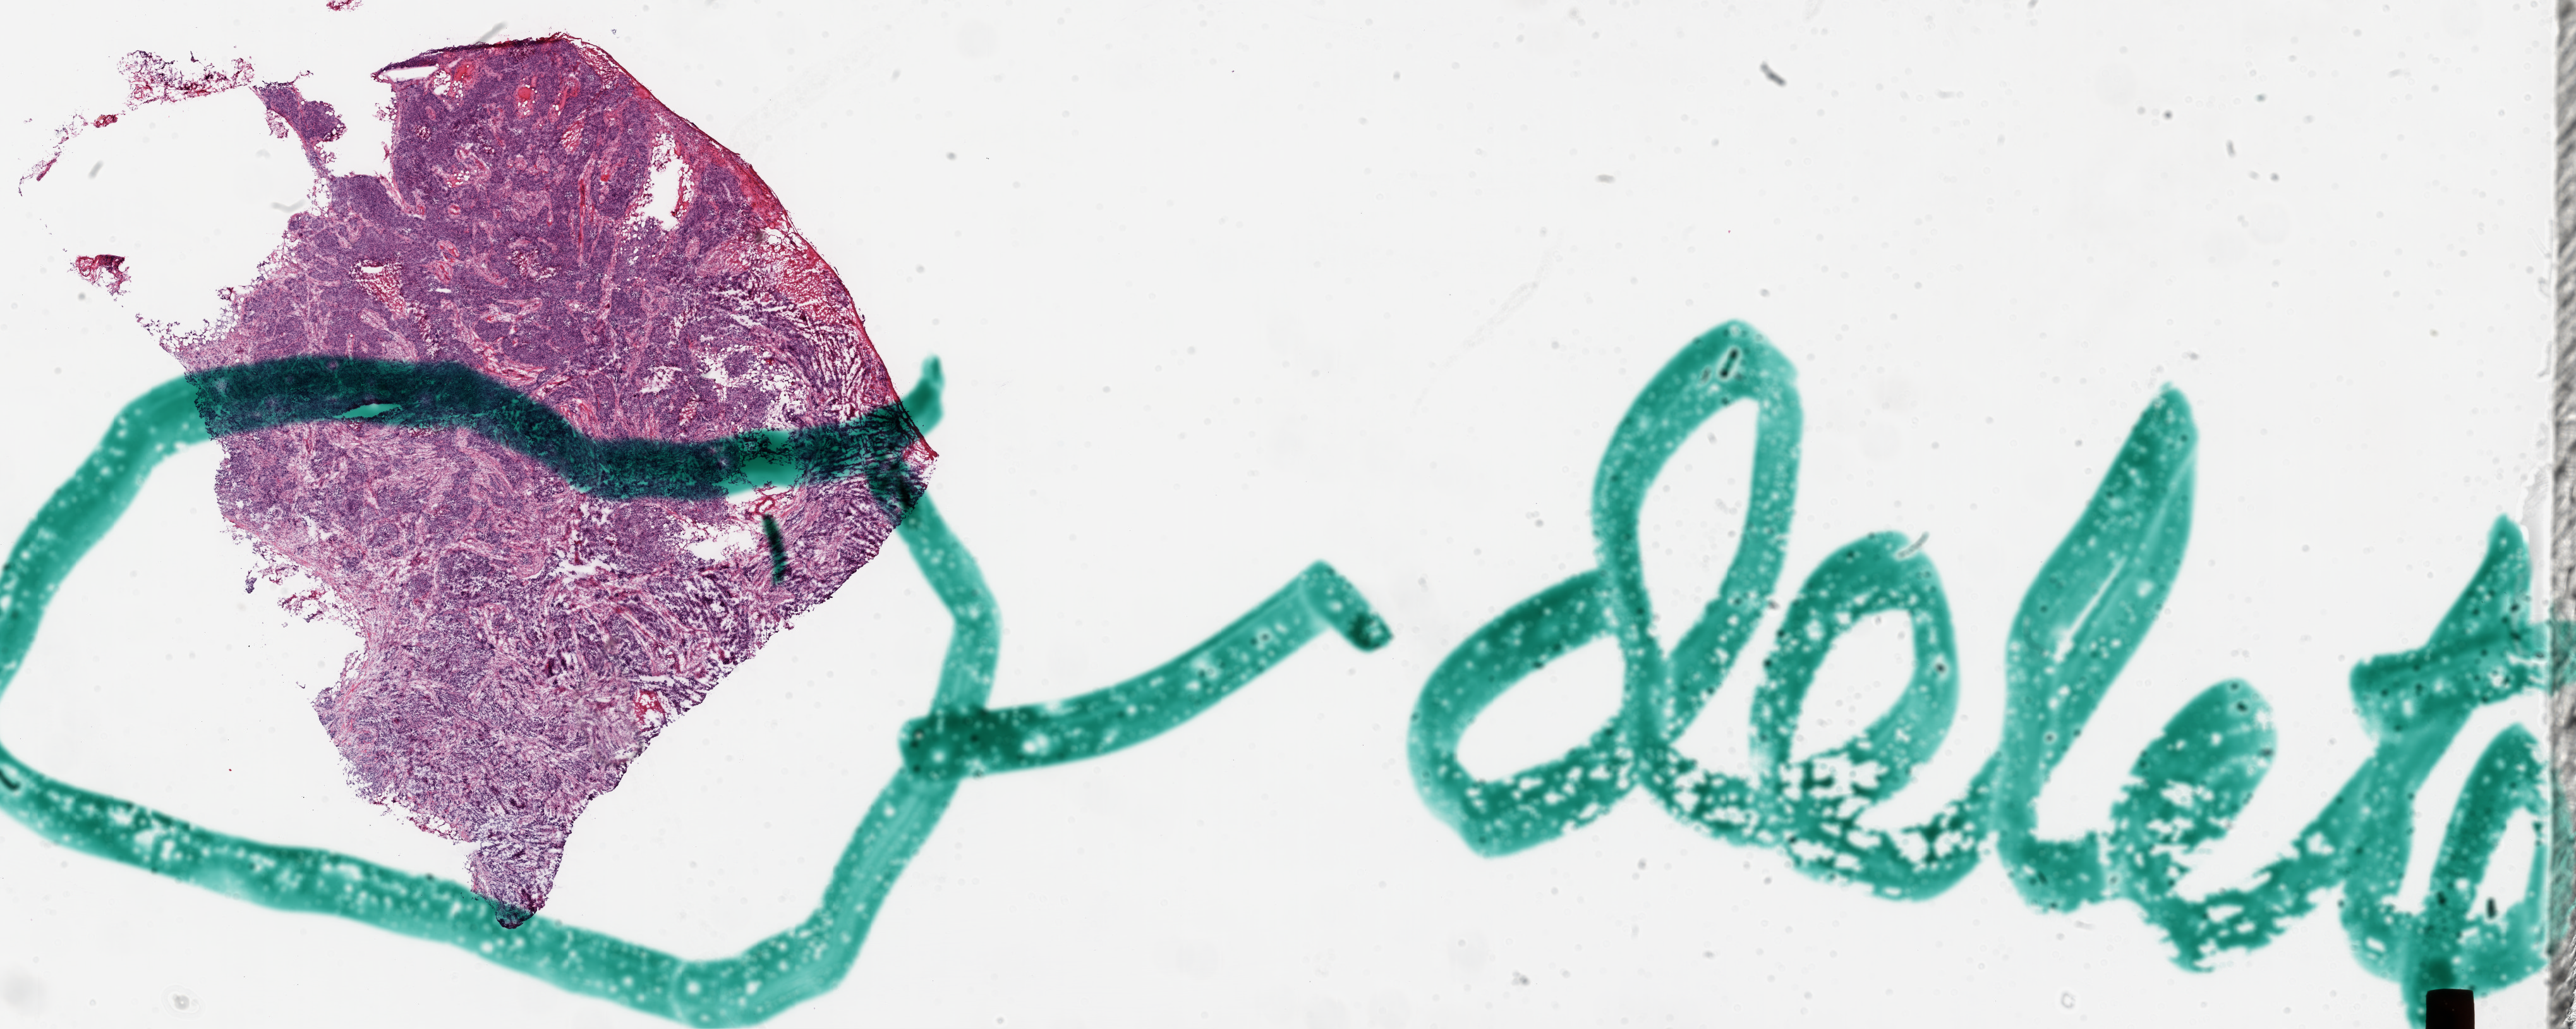
Whole-slide histology image, H&E-stained — whole scanned area (about 32.9 x 13.1 mm) shown as a low-resolution overview; frozen section from the top of the tissue portion; sample: primary tumour, ovary. Female patient; age at initial diagnosis 71 years. Histologic grade: G3 (poorly differentiated). Composition of this section per pathologist review: tumour cells 75%, tumour nuclei 80%, normal cells 20%, stromal cells 1%, necrosis 5%. Inflammatory infiltration, as recorded: lymphocyte infiltration 100%.
Laterality: bilateral. FIGO stage: IIIC. Pathologic diagnosis: Serous cystadenocarcinoma, NOS.